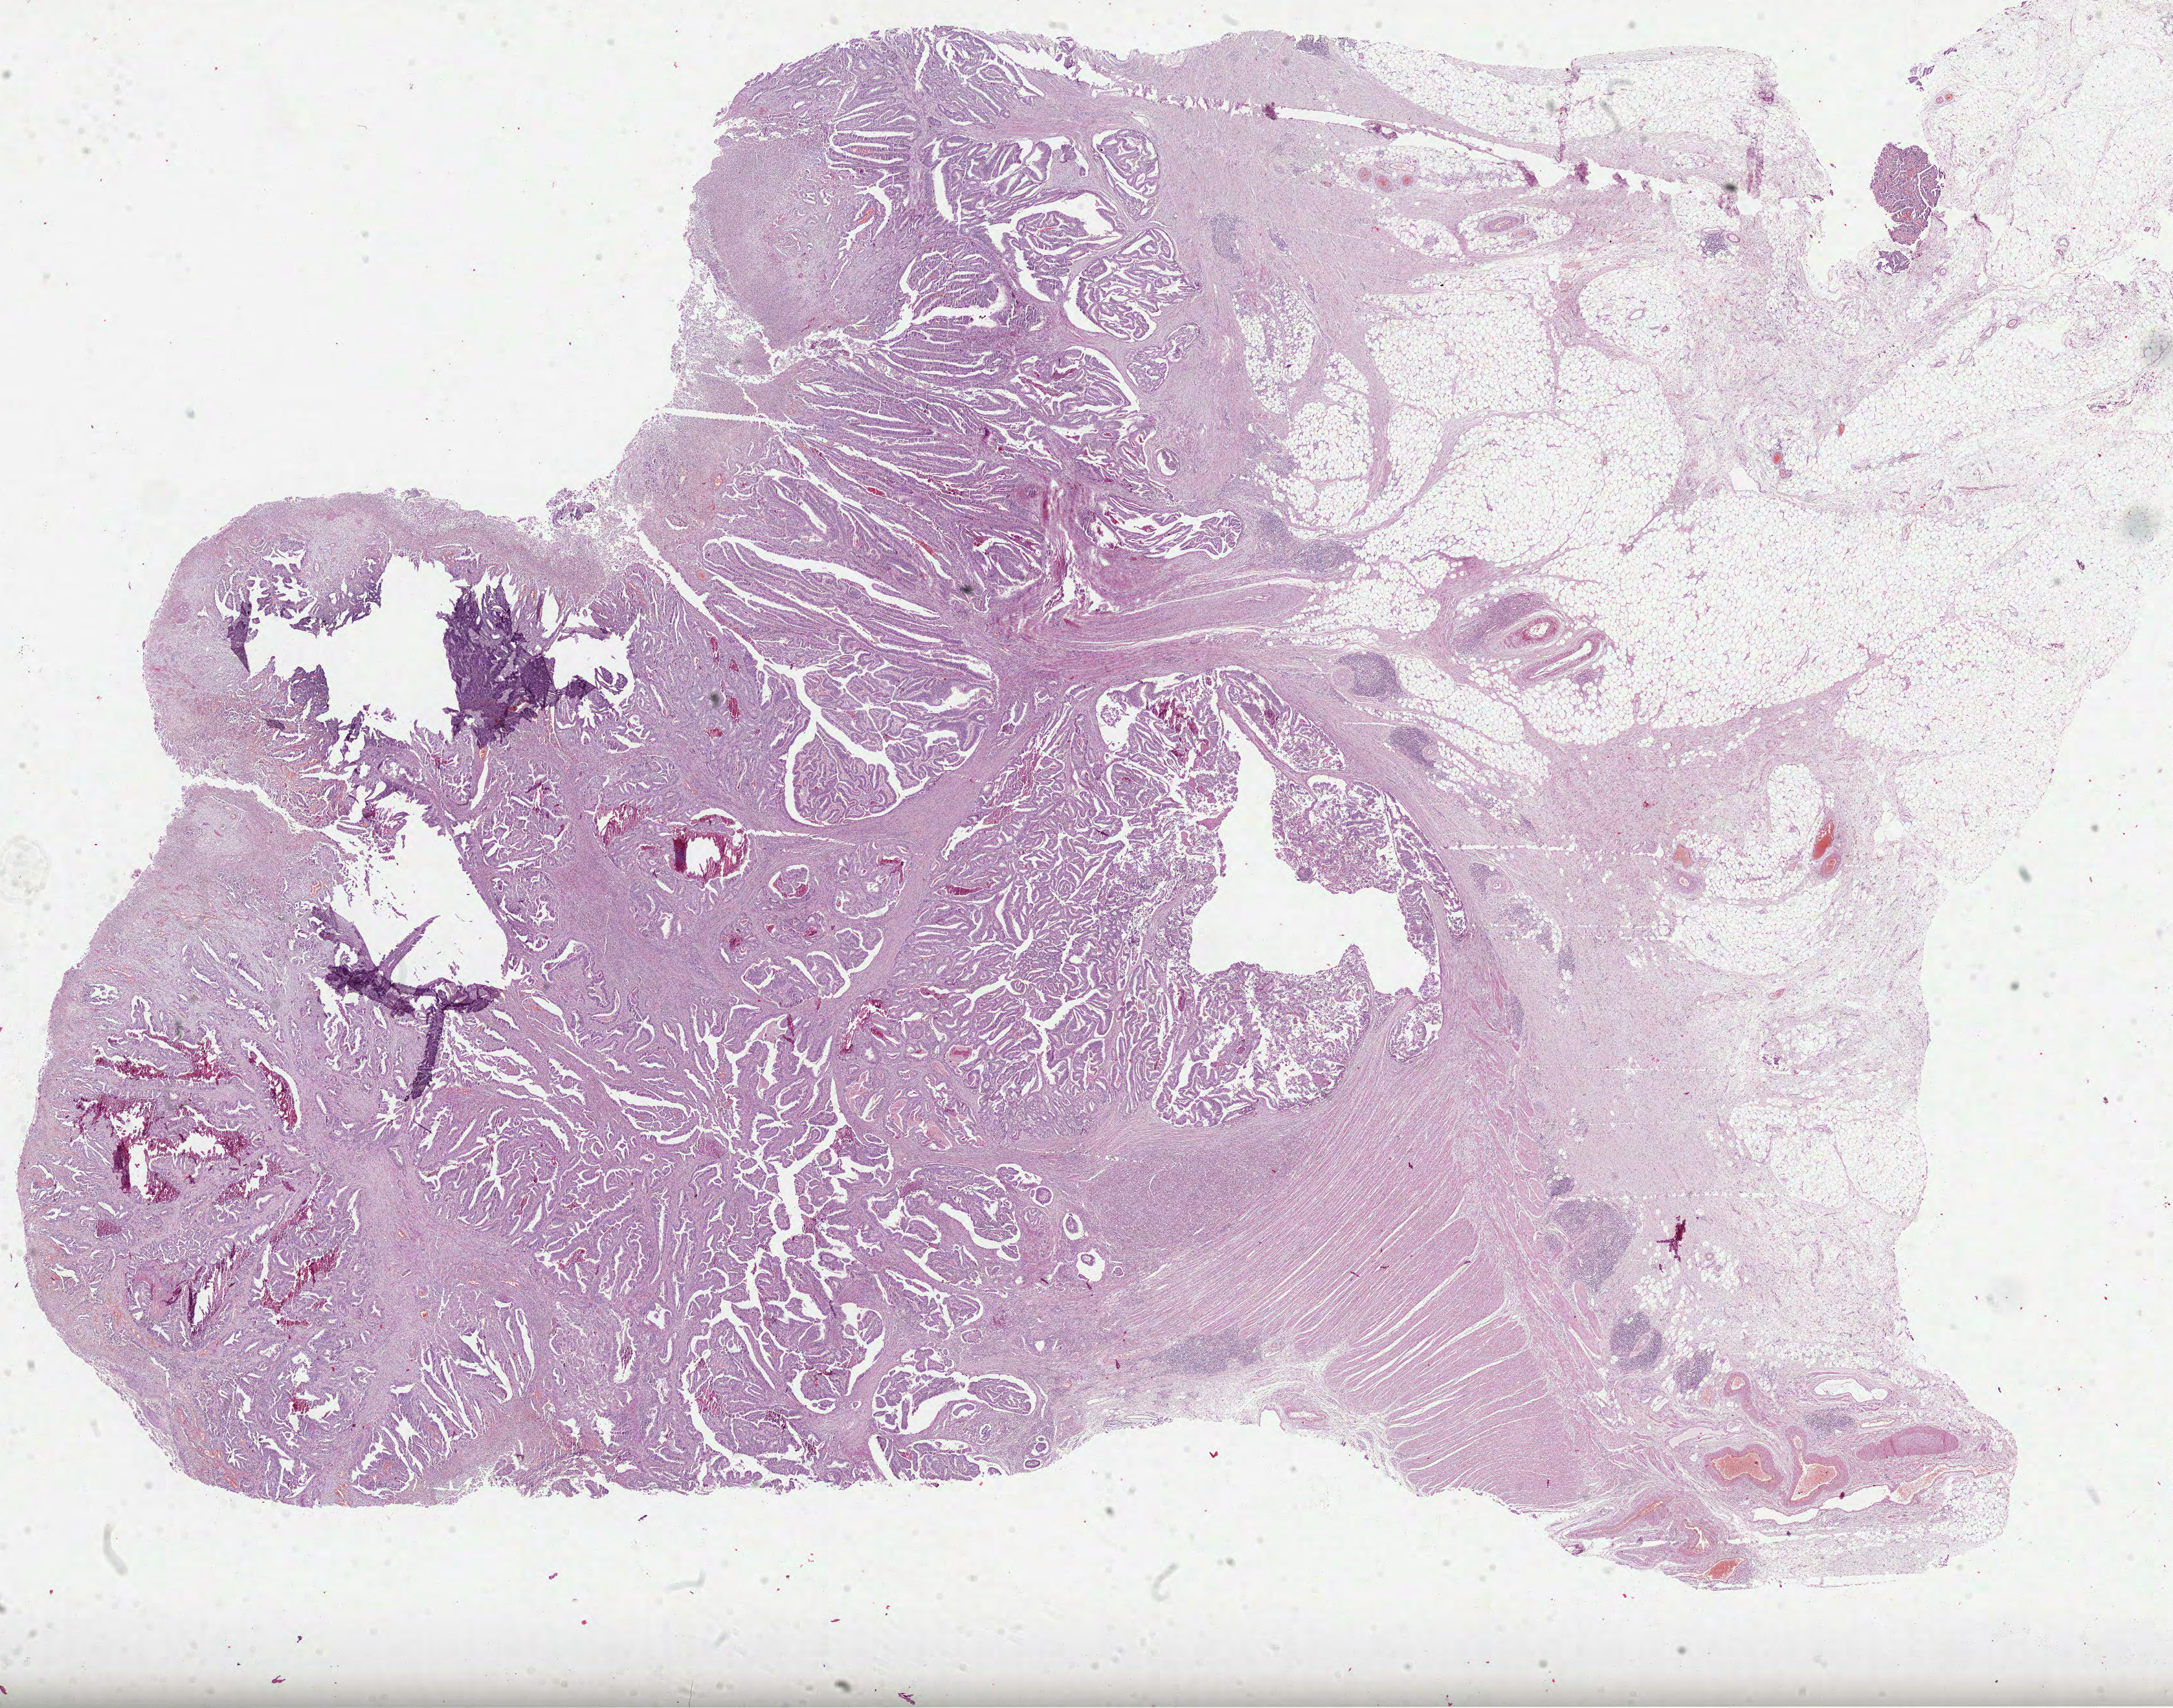
Digitized H&E tissue section (whole slide), shown as a low-resolution overview of the whole scanned area (about 27.1 x 21.3 mm, slide scanned at 40x), FFPE section, primary tumour sample from the rectum. Male patient; age at initial diagnosis 59 years.
Histologic diagnosis: Adenocarcinoma in tubulovillous adenoma.